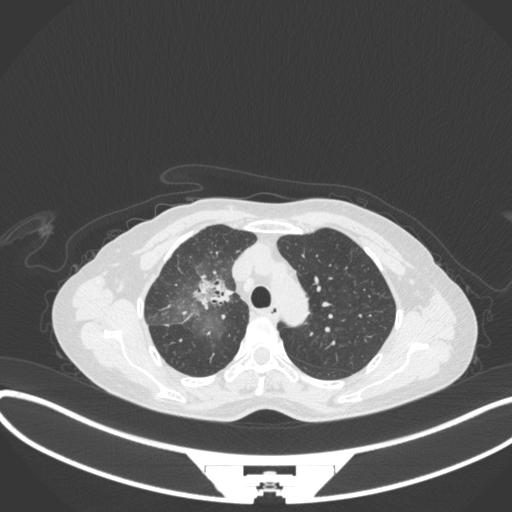
Chest CT, one axial slice. Position 235 of 311 along the scan axis. Lung window (W 1500 / L -600 HU). 1 mm slice thickness. 512 × 512 image matrix. Patient: female, 59 years. Case-level facts recorded for this patient, not image findings: clinical TNM (as recorded): T3 N0 M0.
Annotated regions visible in this slice (rectangle marked by the reading radiologist):
- lung tumour (recorded histology: adenocarcinoma): box from (x=191, y=269) to (x=235, y=314) px